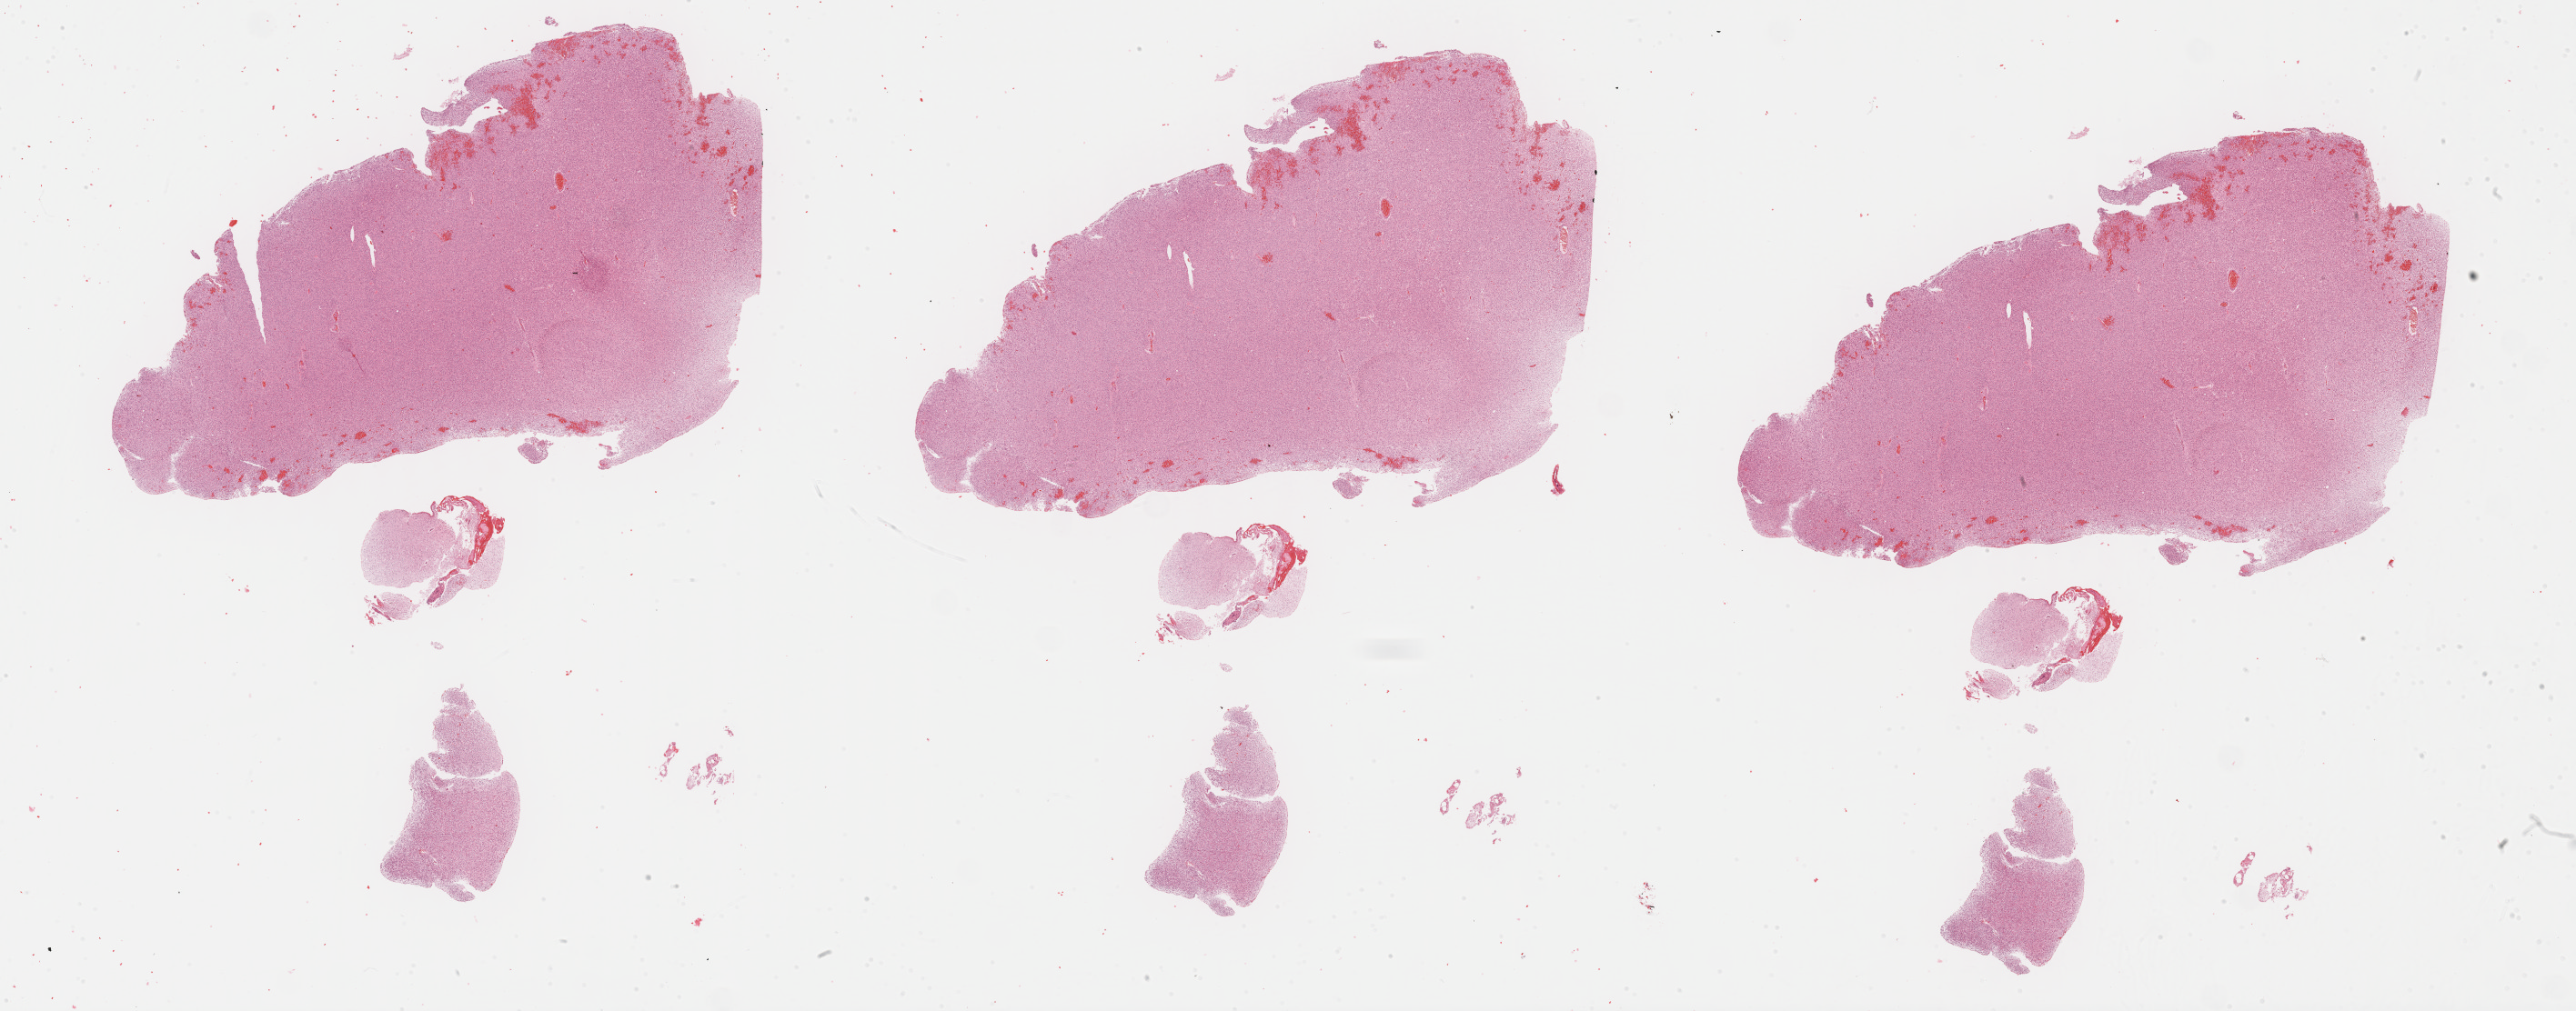
Whole-slide histology image, Hematoxylin and eosin (H&E) stained, shown as a low-resolution overview of the whole scanned area (about 45.8 x 18.0 mm, from a 40x scan). FFPE section. Sample: primary tumour, brain. Female patient; age at initial diagnosis 61 years. Histologic grade: G3 (poorly differentiated).
Laterality: right. Histologic diagnosis: Oligodendroglioma, anaplastic (cerebrum).